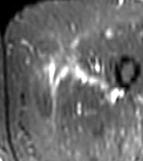
MRI of an extremity soft-tissue mass, one axial slice. Position 10 of 81 along the scan axis. STIR. MR volume resampled by the dataset authors to the PET/CT grid (not the native acquisition matrix). 3.27 mm slice thickness. 143 × 161 image matrix, field of view 140 × 157 mm. Female patient. Case-level facts recorded for this patient, not image findings: histological type: myxofibrosarcoma; grade: intermediate; site of the primary tumour: left thigh.
Annotated regions visible in this slice (expert contour drawn on MRI and transferred to this co-registered scan by the dataset authors):
- gross tumour volume including surrounding oedema: bounding box (x1, y1, x2, y2) in pixels: (40, 56, 111, 96)